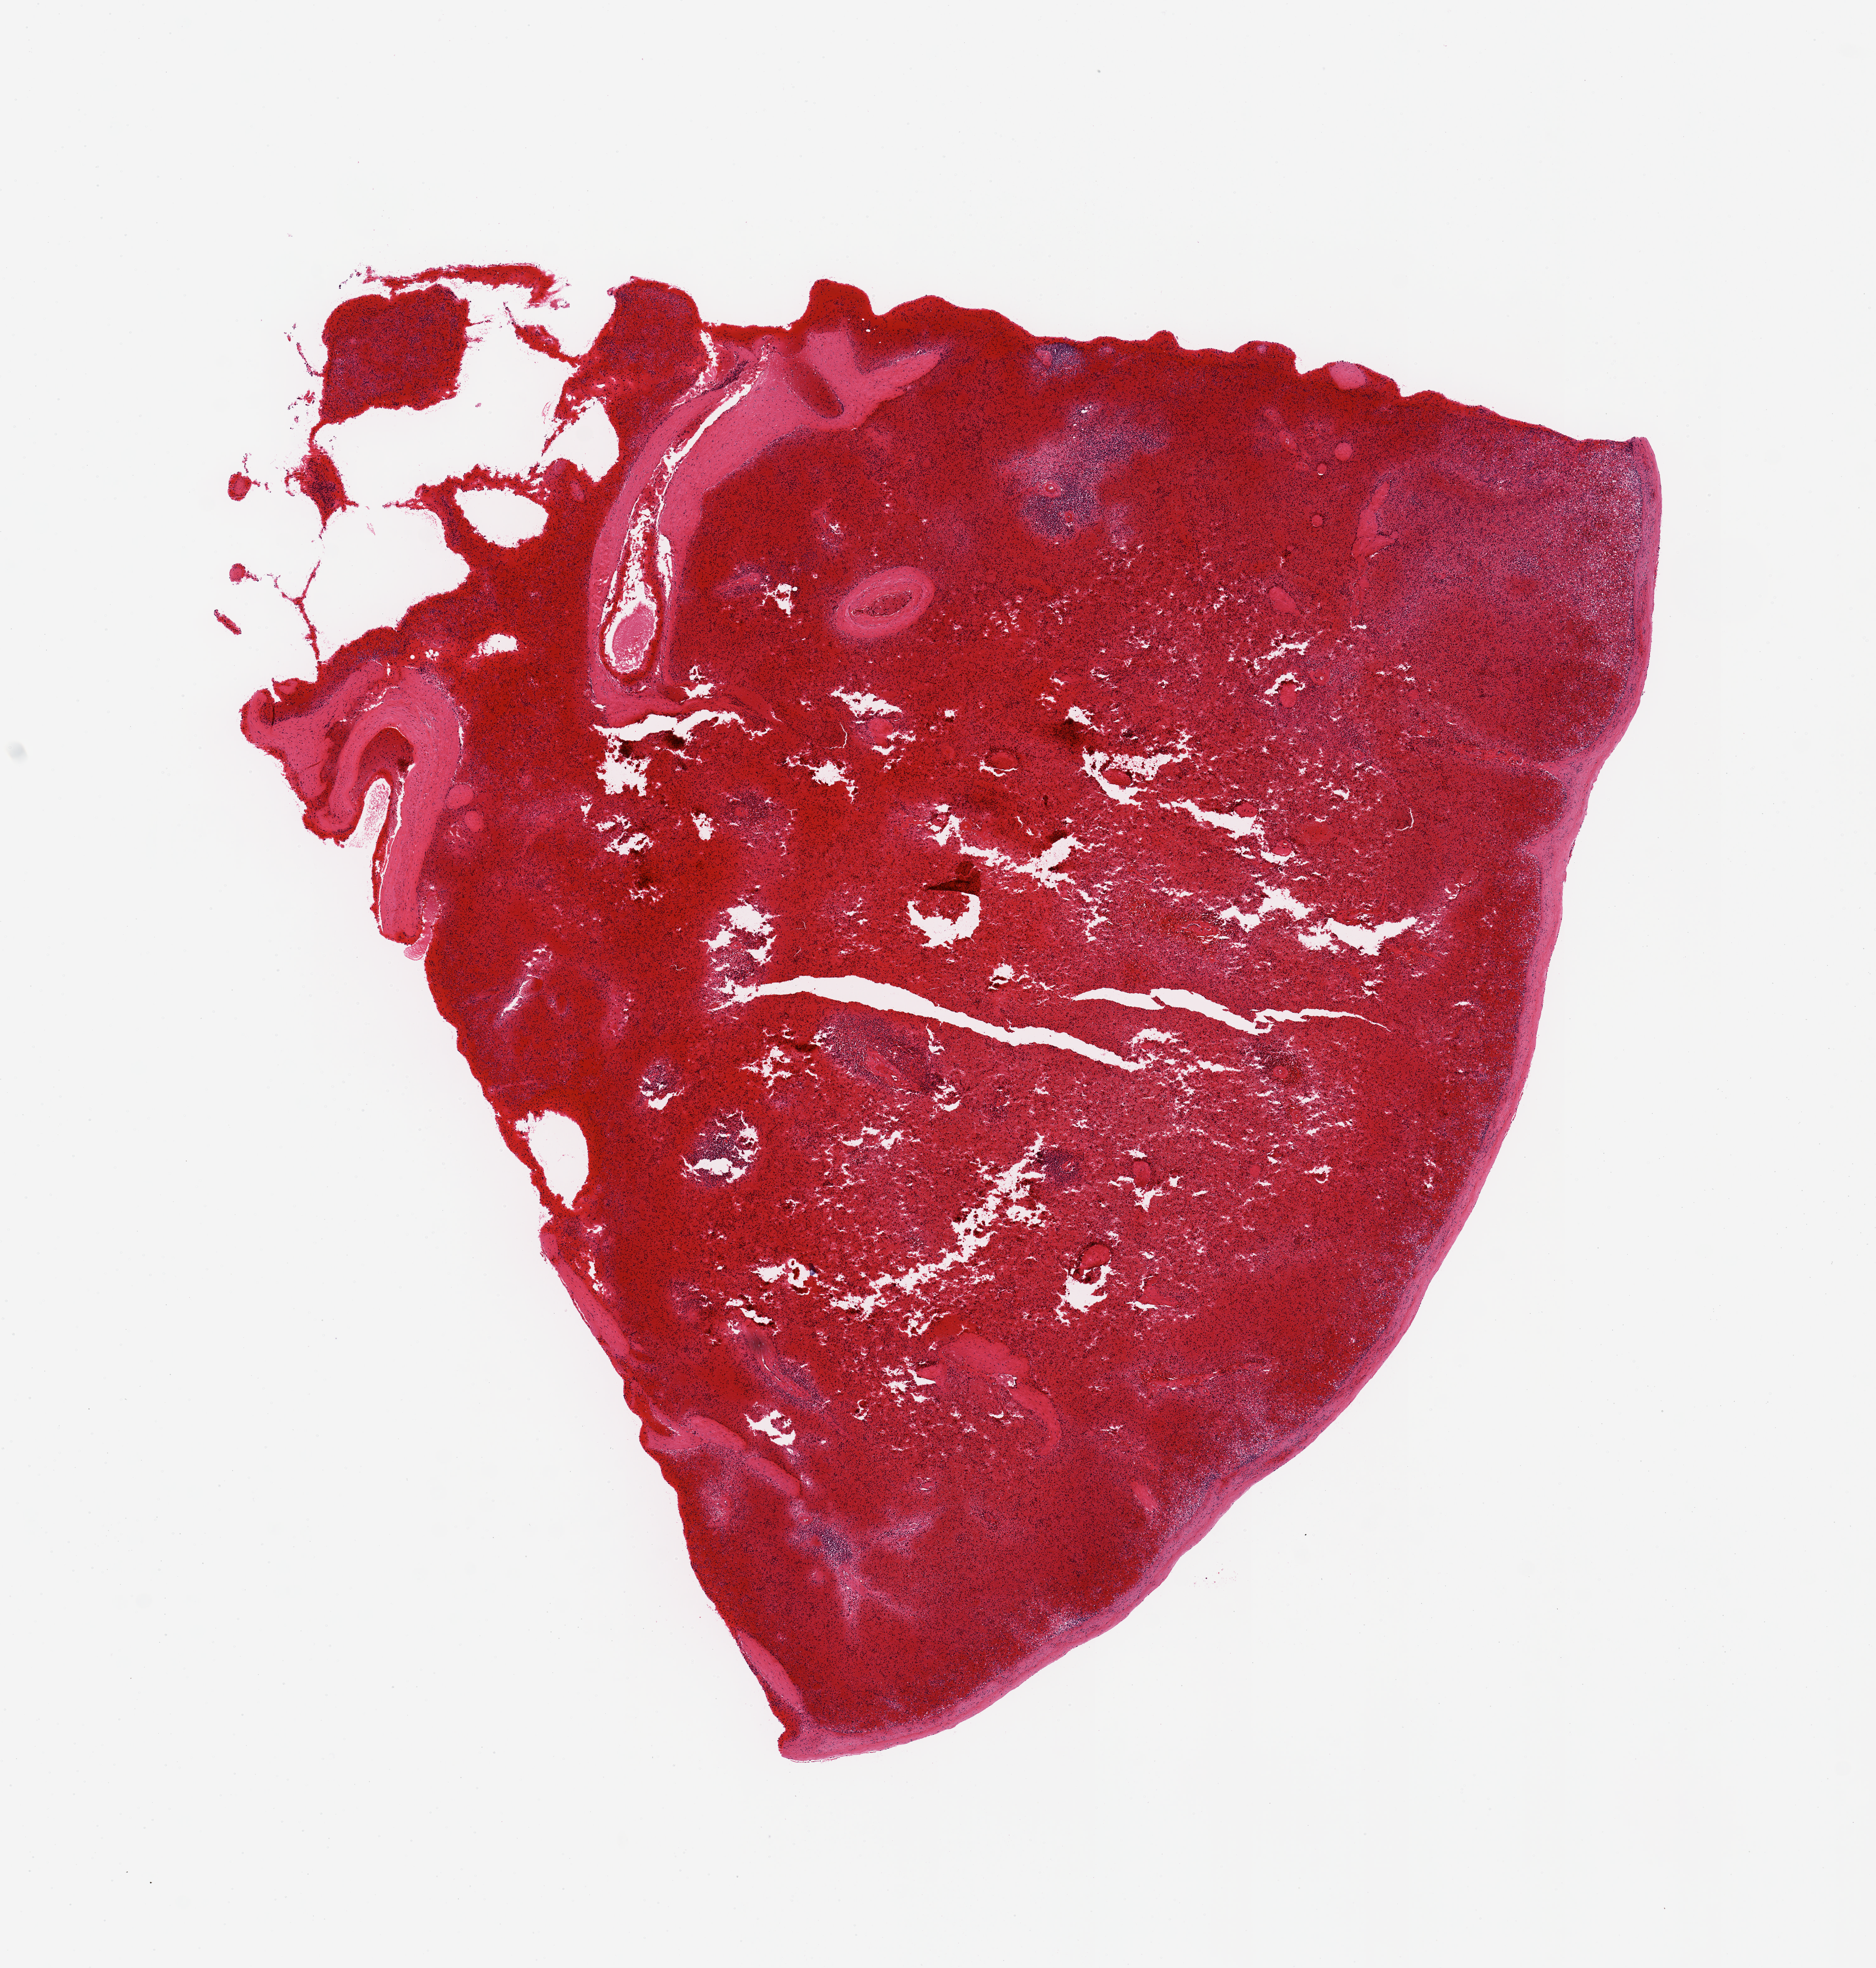
Haematoxylin and eosin whole-slide image, a low-resolution overview of the entire scanned area, about 11.8 x 12.4 mm, PAXgene-fixed paraffin-embedded (PFPE) section, section of spleen (target tissue), tissue donor sample. Donor: male.
- pathologist's review note for this sample: Severe acute passive congestion